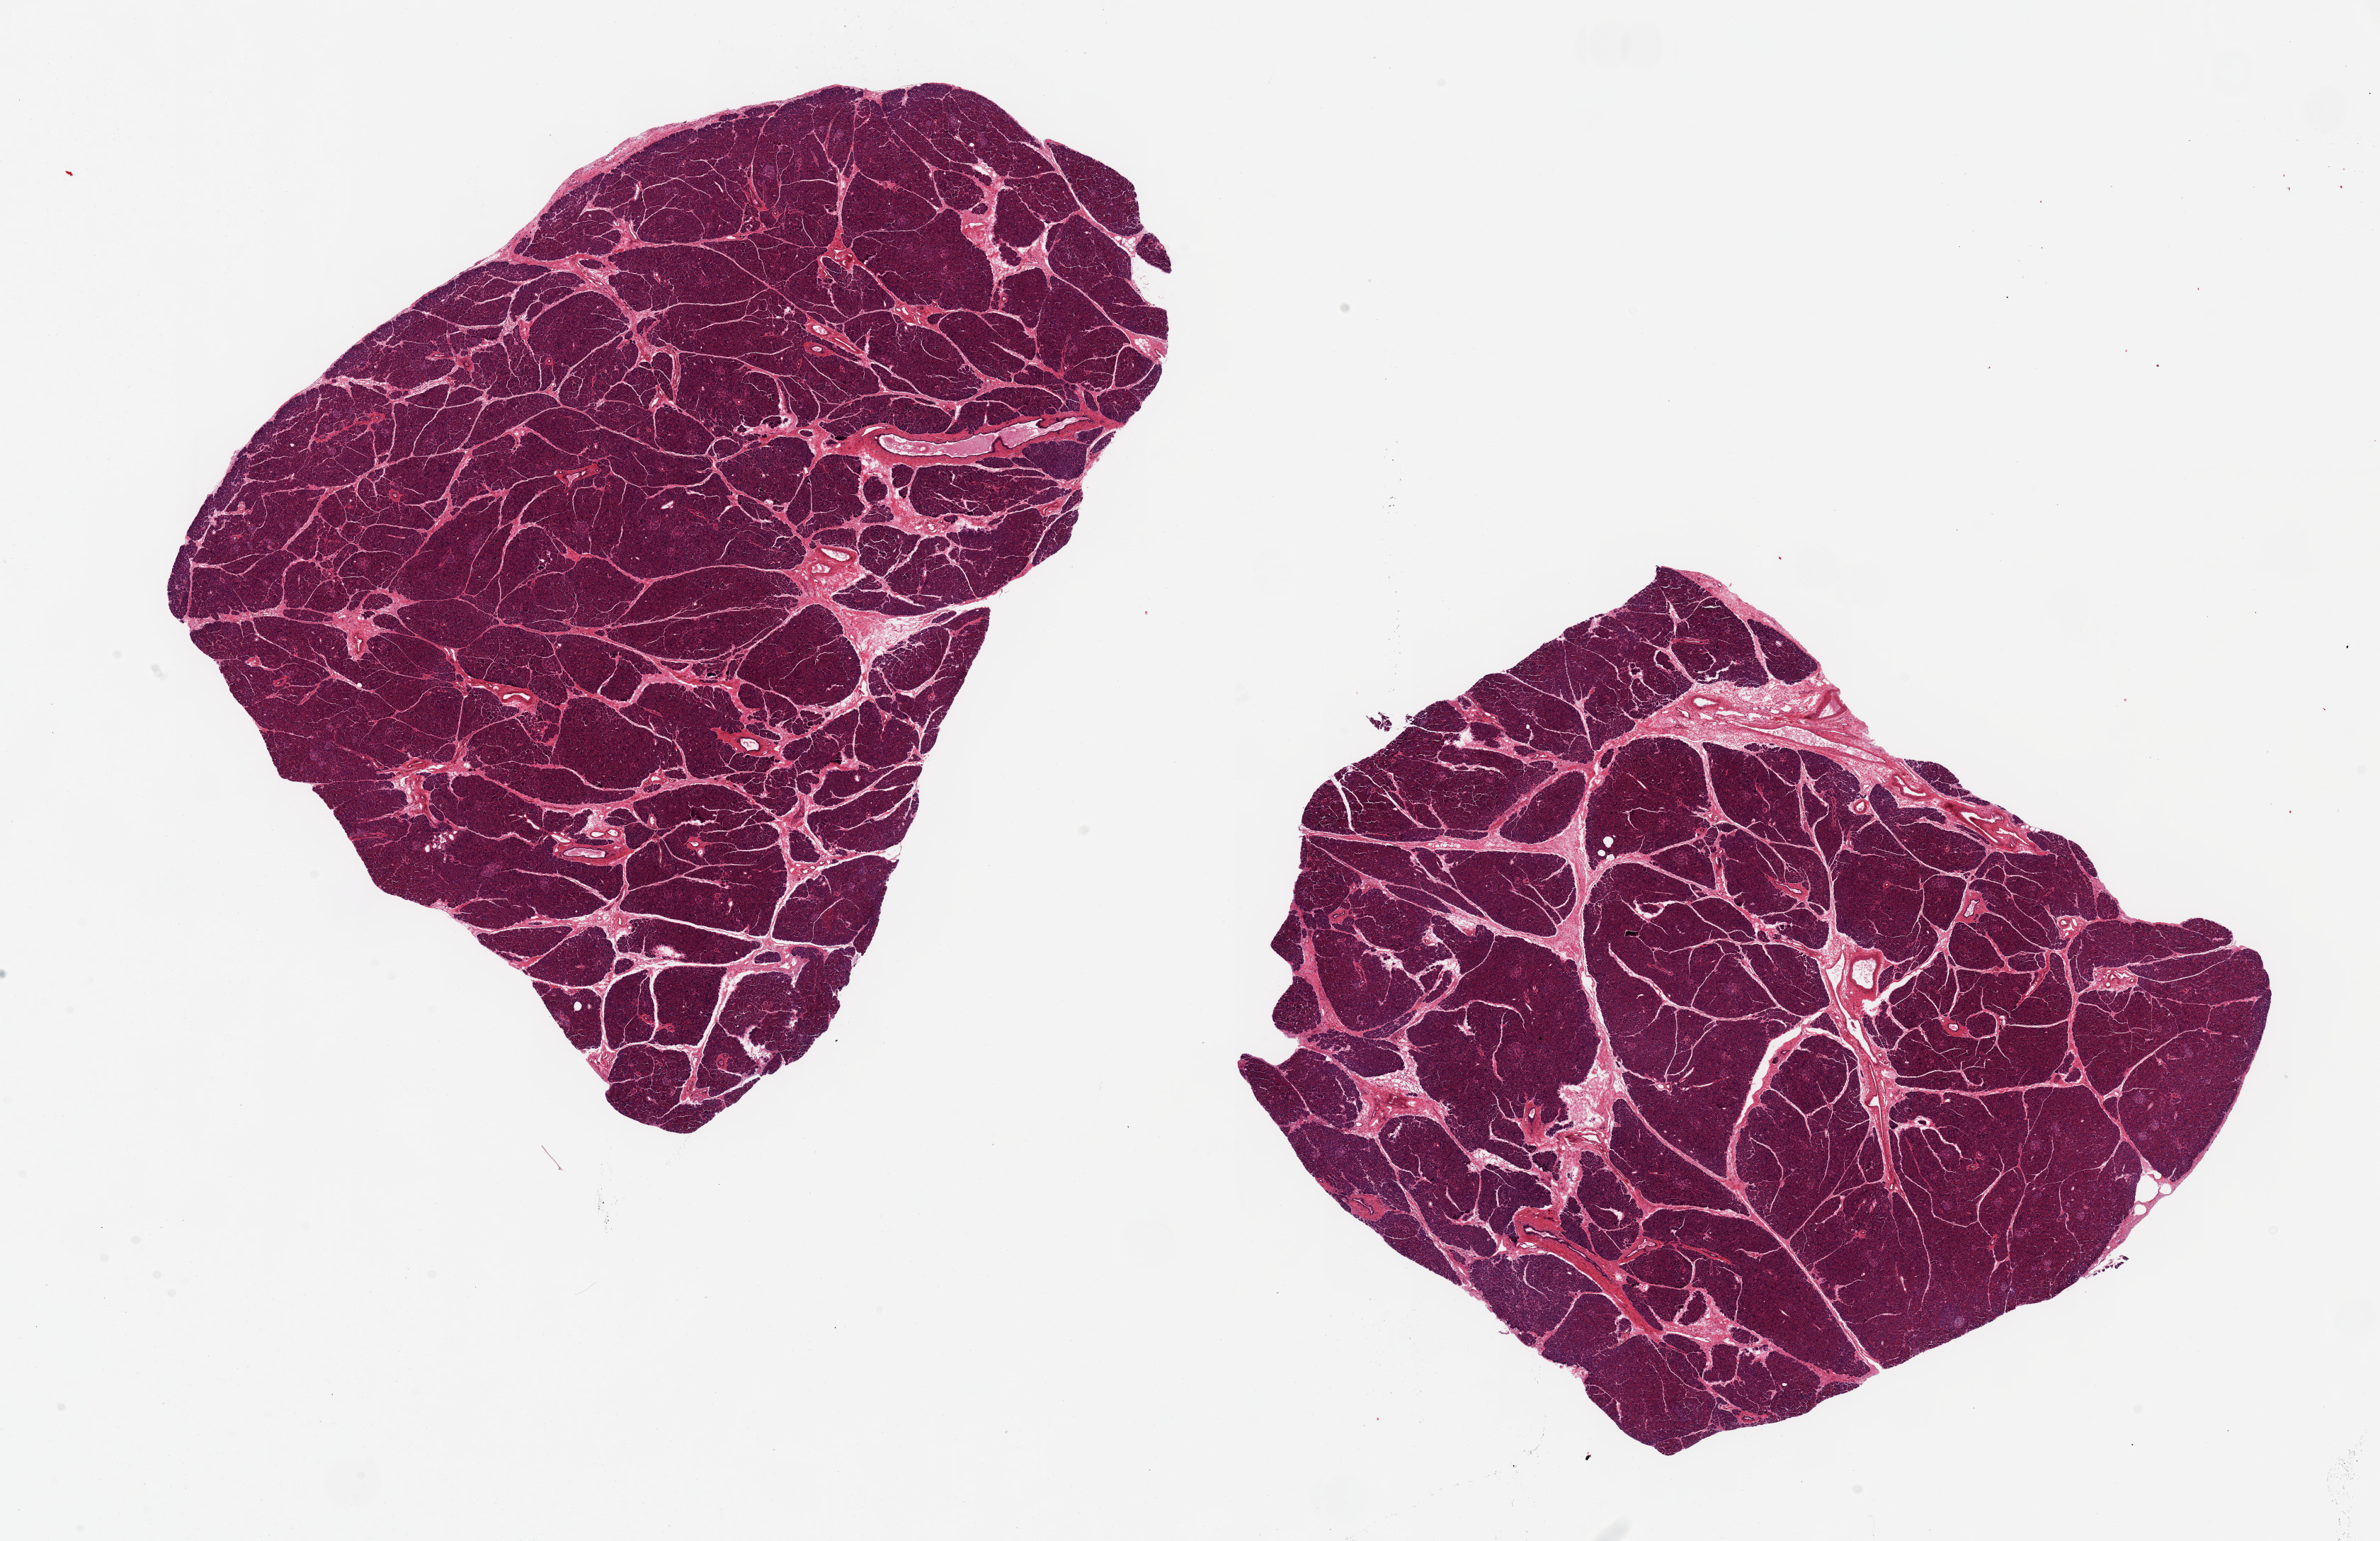
Whole-slide image, hematoxylin and eosin (H&E) stain, brightfield, low-resolution overview of the scanned area, about 26.6 x 17.2 mm (from a 20x scan). PAXgene-fixed paraffin-embedded (PFPE) section. Sampled site (target tissue): pancreas. Donor tissue sample. Donor: female.
Review note (as recorded): 2 pieces, 11x9mm, 9x9mm; well preserved.